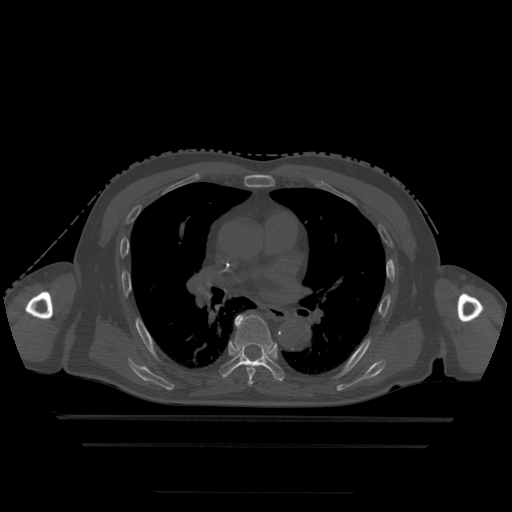
CT including the spine, one axial slice. Slice 305 of 522 in the series (ordered by position). Bone window (W 1800 / L 400 HU). 1.25 mm slice thickness. 512 × 512 image matrix, field of view 436 × 436 mm. Patient age 68 years. From the clinical record (not read from this slice): primary cancer: urothelial.
Outlined on this slice (semi-automatically segmented with operator editing):
- T5 vertebra: box from (x=248, y=379) to (x=253, y=387) px
- T6 vertebra: (x=247, y=367)–(x=255, y=379)
- T7 vertebra: (x=220, y=315)–(x=285, y=382)